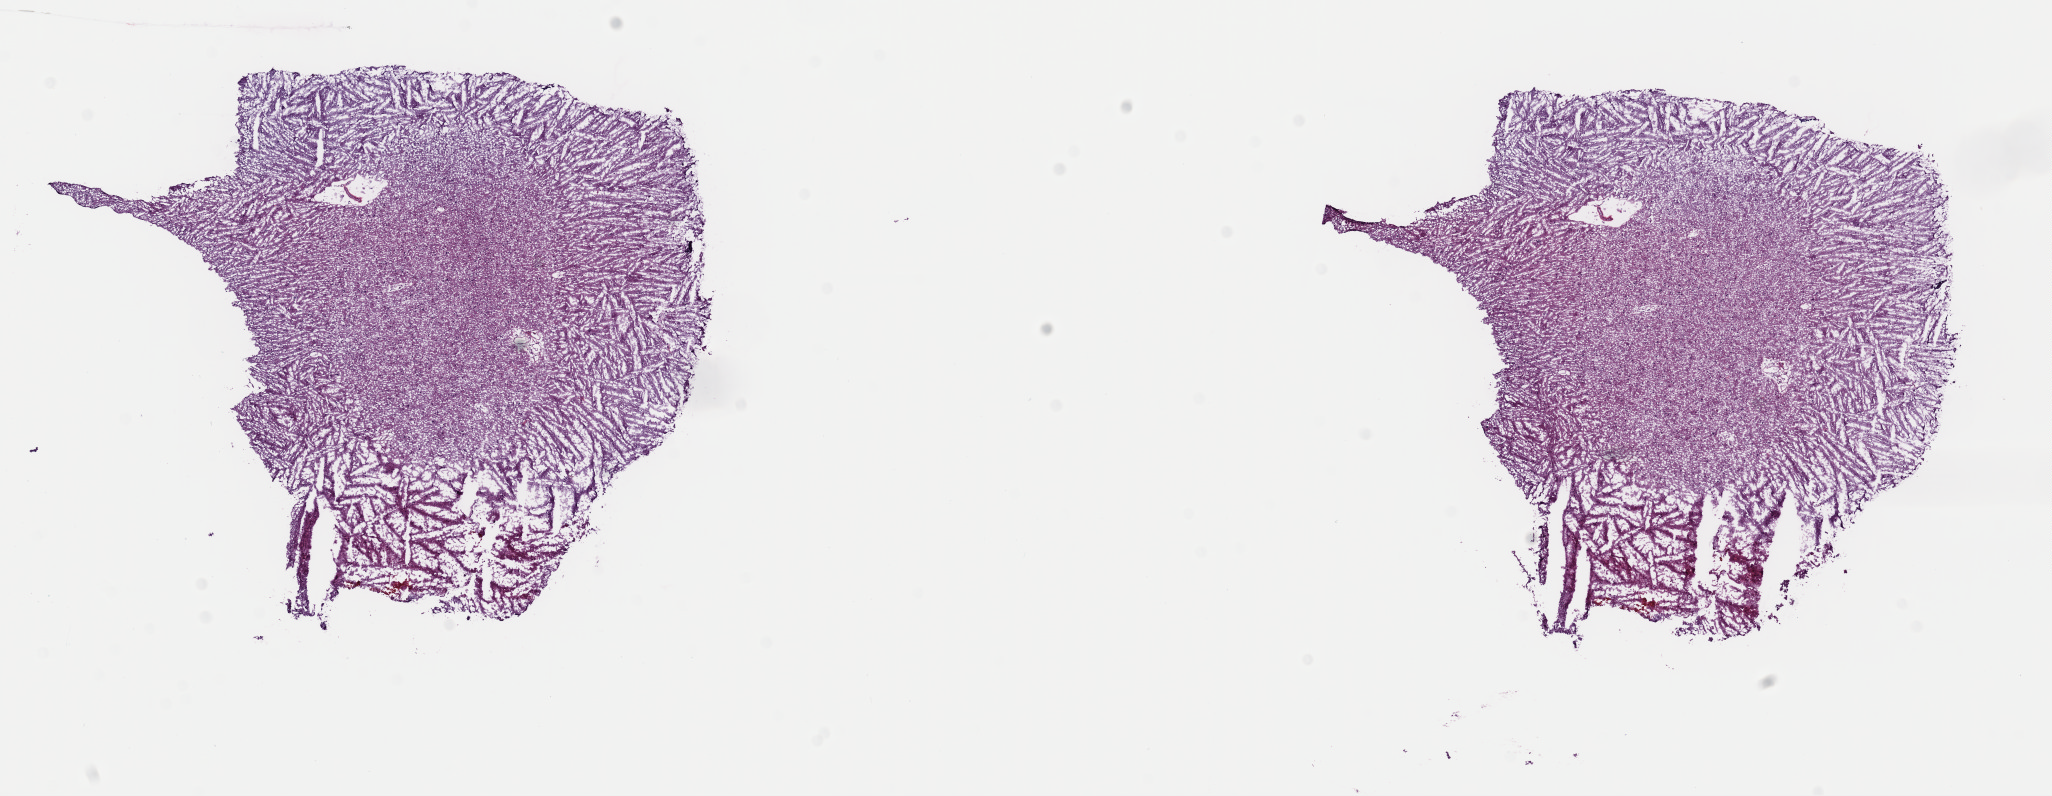
H&E whole-slide image, a low-resolution overview of the entire scanned area, about 16.2 x 6.3 mm (acquisition: 40x scan), frozen section from the top of the tissue portion, primary tumour sample from the brain. Female, age 74 years at initial diagnosis. Histologic grade: G2 (moderately differentiated). Composition of this section per pathologist review: tumour cells 30%, tumour nuclei 70%, normal cells 10%, stromal cells 60%, necrosis 0%. Infiltration values recorded for this section: lymphocyte infiltration 0%, monocyte infiltration 0%, neutrophil infiltration 0%.
* pathologic diagnosis: Mixed glioma (cerebrum)
* laterality: right